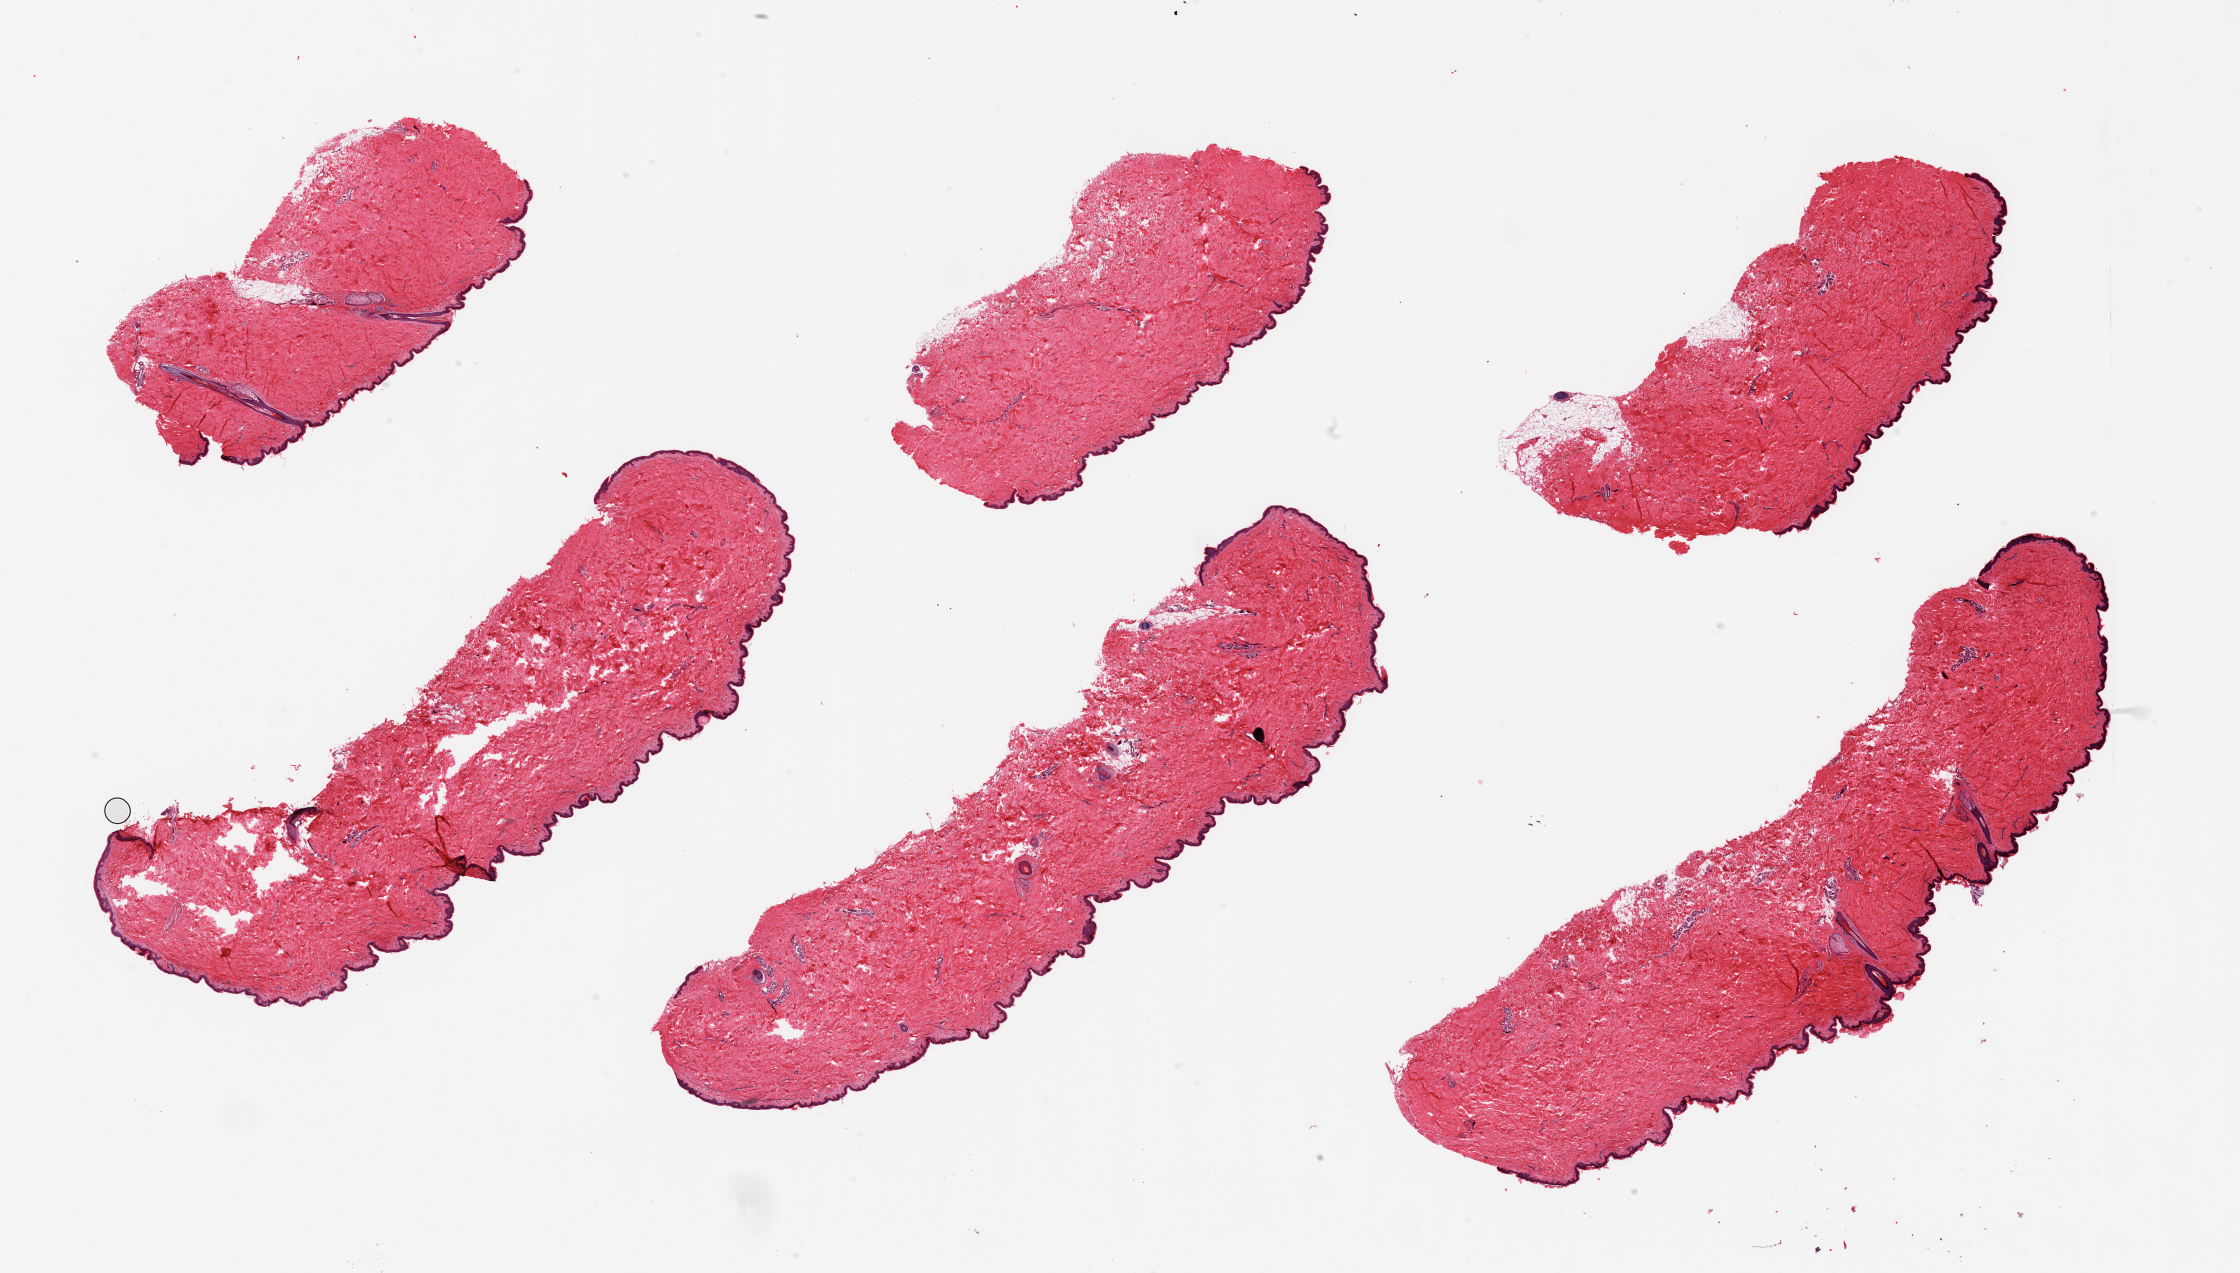
Whole-slide image, hematoxylin and eosin (H&E) stain — whole scanned area (about 35.4 x 20.1 mm) shown as a low-resolution overview. PAXgene-fixed paraffin-embedded (PFPE) section. Section of skin of suprapubic region (target tissue). Donor tissue sample. Donor sex: male.
- review note (as recorded): 6 pieces, no adherent fat, squamous epithelium is ~40-50 microns